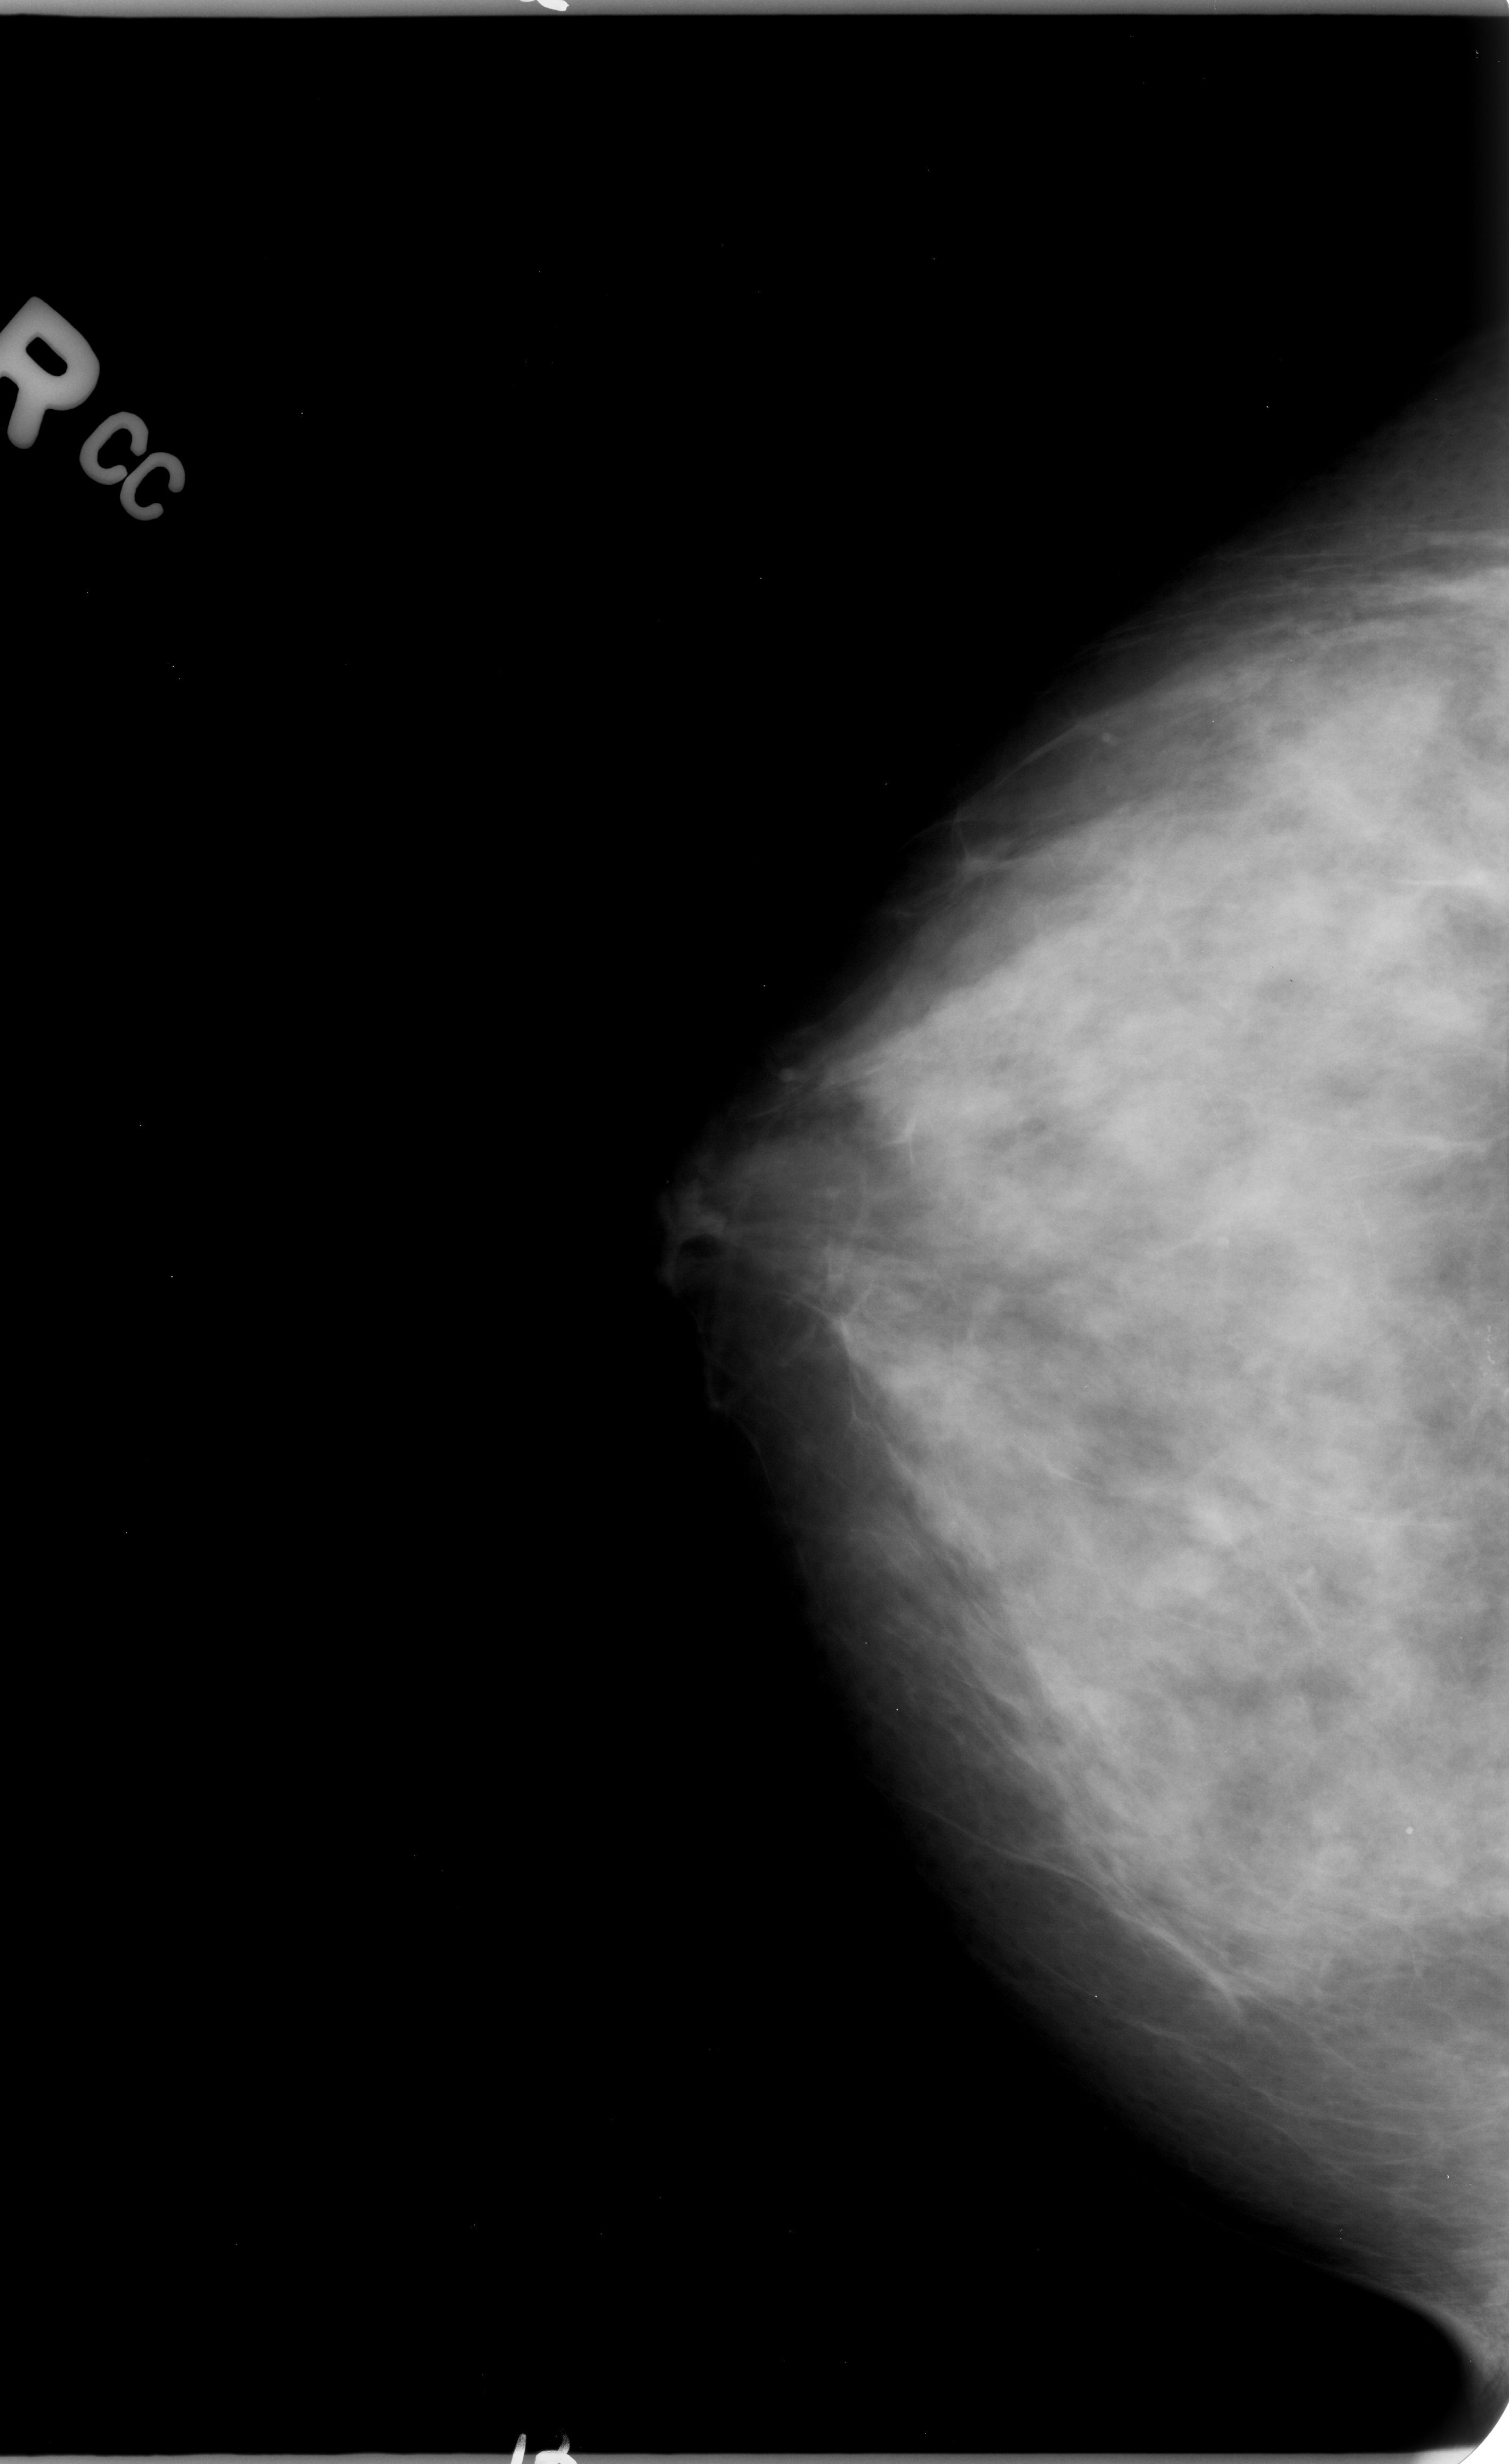
Mammogram (digitized film). Right breast. CC view. Breast composition: extremely dense (BI-RADS density category 4 of 4). 1509 × 2464 image matrix.
Expert-marked regions of interest on this image (one box per marked abnormality):
- calcifications, morphology pleomorphic, distribution clustered; BI-RADS assessment category 4; subtlety rating 4 on a 1 (subtle) to 5 (obvious) scale; pathology (as recorded): malignant: bounding box <1402,1287,1506,1472> (left, top, right, bottom; pixels)